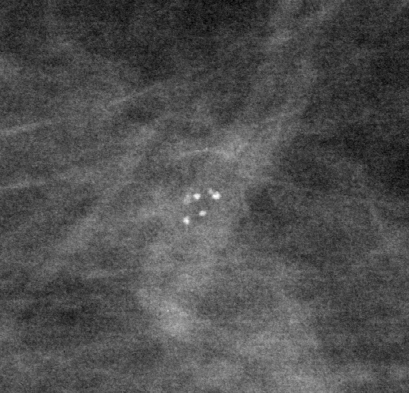
Region of interest cut from a scanned film mammogram (one marked finding); left breast; MLO view.
- Finding: calcifications, morphology punctate, distribution clustered; BI-RADS assessment category 3; subtlety rating 4 on a 1 (subtle) to 5 (obvious) scale; pathology result (as recorded, not read from the image): benign.